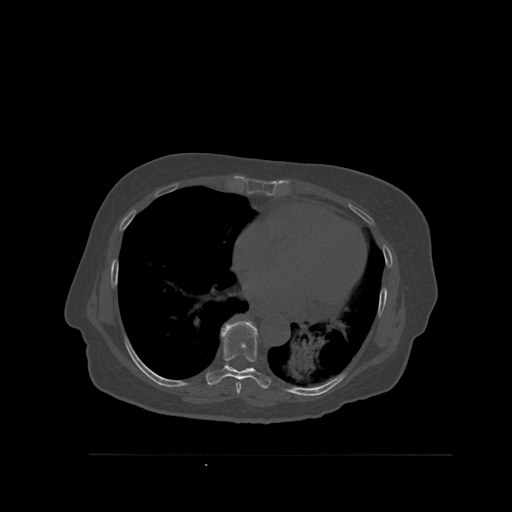
CT including the spine, one axial slice. Slice 351 of 527 in the series (ordered by position). Bone window (W 1800 / L 400 HU). 512 × 512 image matrix, field of view 470 × 470 mm. Female patient, age 73 years. Case-level facts recorded for this patient, not image findings: primary cancer: breast; vertebrae with lytic lesions (as recorded): L2.
Structures marked on this image (semi-automatically segmented with operator editing):
- T7 vertebra: bounding box (x1, y1, x2, y2) in pixels: (235, 379, 241, 395)
- T8 vertebra: (206, 321, 271, 389)
- T9 vertebra: (225, 323, 227, 325)